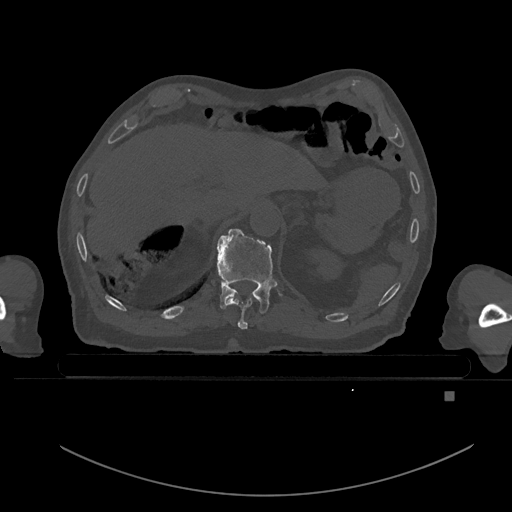
CT including the spine, one axial slice. Position 50 of 969 along the scan axis. Bone window (W 1800 / L 400 HU). 0.5 mm slice thickness. 512 × 512 image matrix, field of view 456 × 456 mm. Patient: male, 82 years. Case-level facts recorded for this patient, not image findings: primary cancer: prostate.
Annotated regions visible in this slice (semi-automatically segmented with operator editing):
- T10 vertebra: box from (x=226, y=297) to (x=254, y=330) px
- T11 vertebra: (x=216, y=228)–(x=277, y=314)